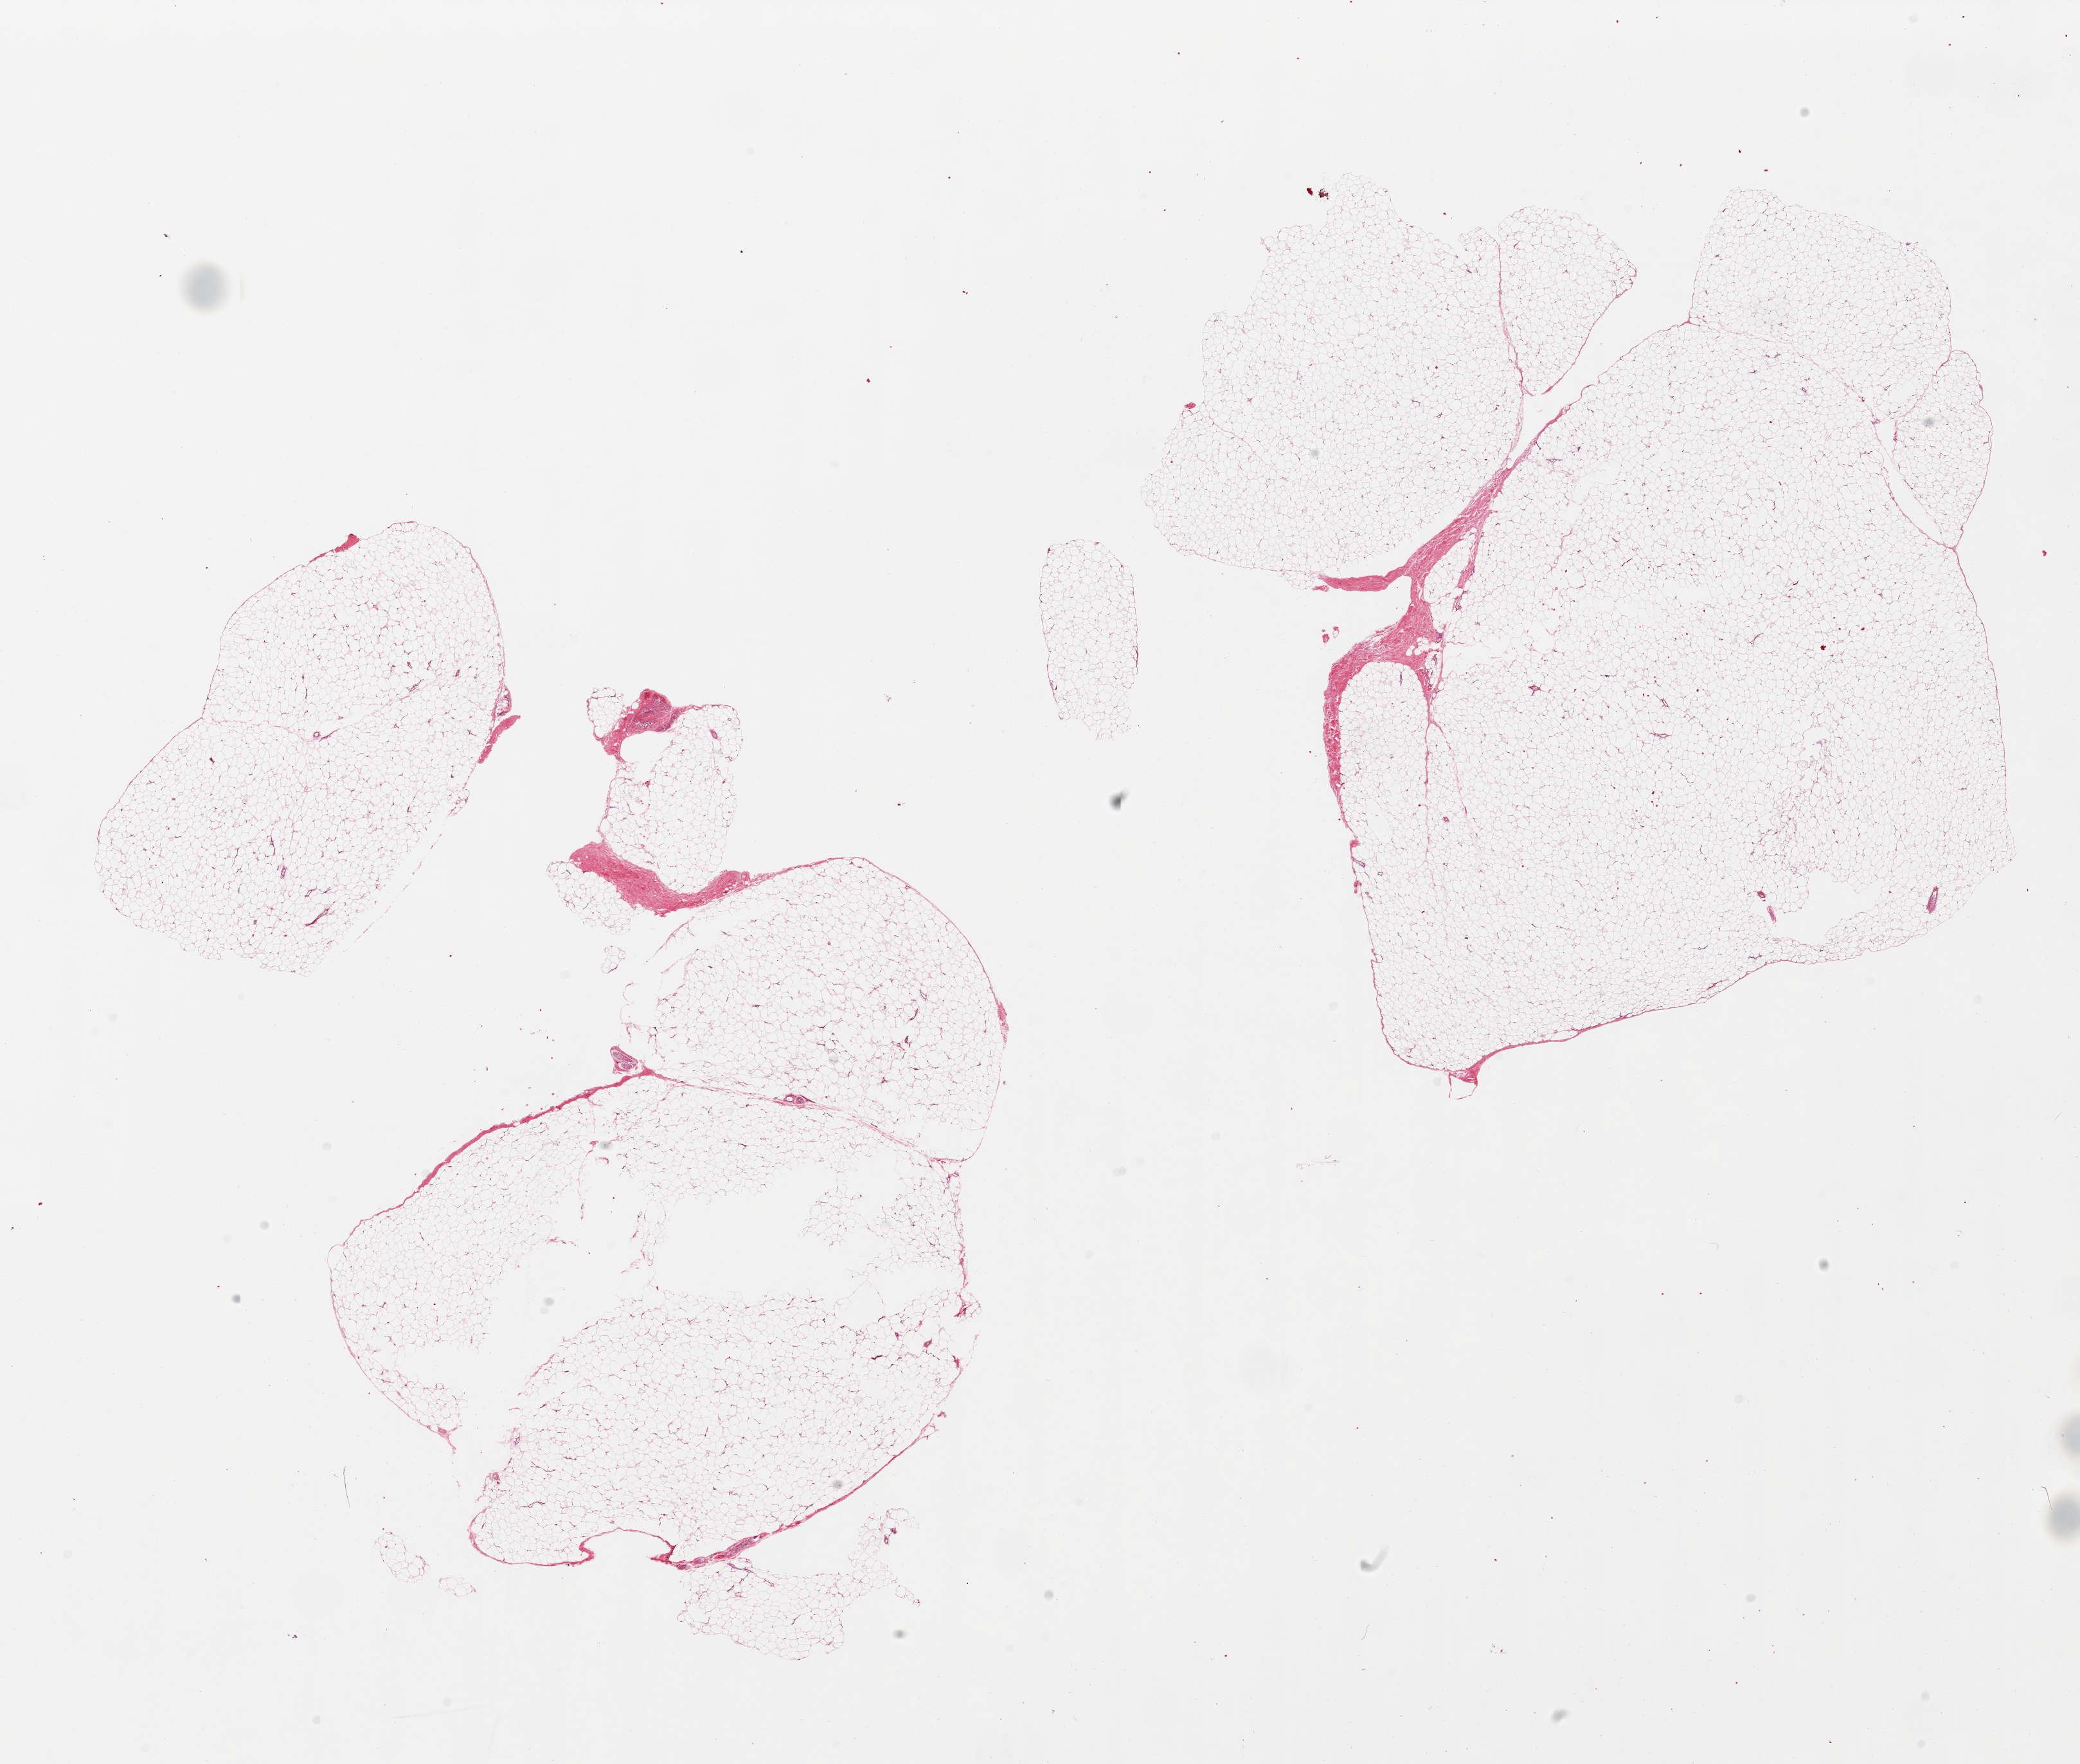
Whole-slide image, haematoxylin and eosin stain, a low-resolution overview of the entire scanned area, about 25.6 x 21.7 mm, PAXgene-fixed, paraffin-embedded tissue, sampled site (target tissue): adipose tissue, donor tissue sample. Male donor.
• reviewer comment on this tissue sample: 3 pieces, scant fibrous tissue, central defect (? incomplete fixation)